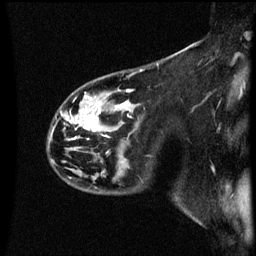
Breast MRI (dynamic contrast-enhanced), one sagittal slice. Position 43 of 60 along the scan axis. Dynamic contrast-enhanced series, image 2 of 3 at this slice position (ordered by acquisition). 1.5 T. TE 4.2 ms, TR 8.9 ms. 2 mm slice thickness. 256 × 256 image matrix, field of view 200 × 200 mm. Patient: female, 44 years. Case-level facts recorded for this patient, not image findings: setting: breast cancer imaged before/during neoadjuvant chemotherapy; receptor status: HR-positive, HER2-negative.
Annotated regions visible in this slice (semi-automatic segmentation, software-assisted and operator-edited):
- analysis volume of interest (the breast-tissue region the enhancement analysis was run in; not a lesion): bounding box (x1, y1, x2, y2) in pixels: (48, 78, 140, 189)
- tumour enhancement mask (voxels above the 70 % enhancement threshold inside the analysis volume of interest): (70, 90, 131, 141)